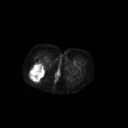
FDG PET of an extremity soft-tissue mass (from a PET/CT study), one axial slice. Slice 50 of 267 in the series (ordered by position). 128 × 128 image matrix, field of view 700 × 700 mm. Patient: female, 70 years. From the clinical record (not read from this slice): histological type: synovial sarcoma; grade: intermediate; site of the primary tumour: right buttock.
Outlined on this slice (expert contour drawn on MRI and transferred to this co-registered scan by the dataset authors):
- gross tumour volume including surrounding oedema: bounding box [x1, y1, x2, y2] px = [29, 63, 45, 81]
- gross tumour volume (mass): [29, 63, 45, 81]